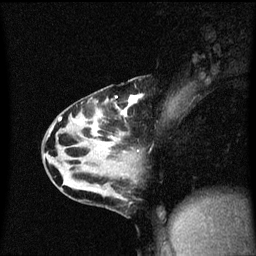
Breast MRI (dynamic contrast-enhanced), one sagittal slice; position 26 of 60 along the scan axis; dynamic contrast-enhanced series, image 2 of 3 at this slice position (ordered by acquisition); 1.5 T; TE 4.2 ms, TR 8.4 ms; 2 mm slice thickness; 256 × 256 image matrix, field of view 200 × 200 mm. Female patient, age 32 years.
Structures marked on this image (semi-automatically segmented with operator editing):
- analysis volume of interest (the breast-tissue region the enhancement analysis was run in; not a lesion): box from (x=55, y=78) to (x=174, y=167) px
- tumour enhancement mask (voxels above the 70 % enhancement threshold inside the analysis volume of interest): (x=59, y=96)–(x=142, y=151)